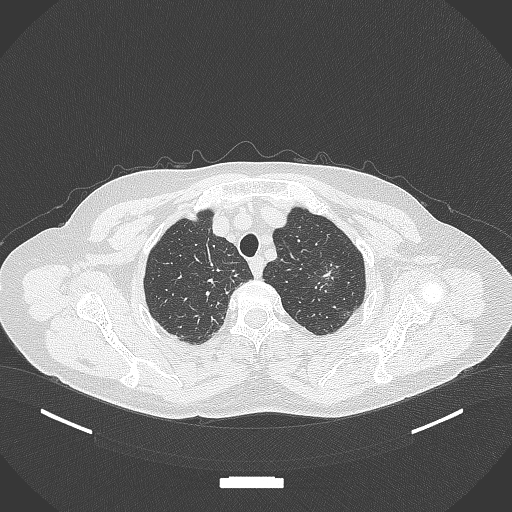
Chest CT, one axial slice. Slice 308 of 369 in the series (ordered by position). Lung window (W 1500 / L -600 HU). 1 mm slice thickness. 512 × 512 image matrix. Patient: female, 64 years. Case-level facts recorded for this patient, not image findings: clinical TNM (as recorded): T1c N0 M0; histopathological grade: G1.
Structures marked on this image (rectangle marked by the reading radiologist):
- lung tumour (recorded histology: adenocarcinoma): bounding box (x1, y1, x2, y2) in pixels: (307, 249, 343, 298)